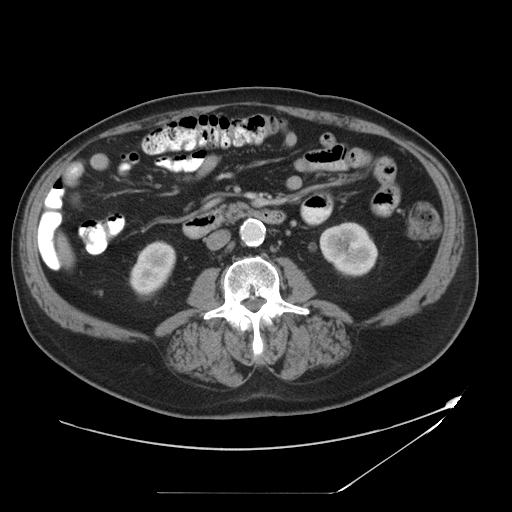
Contrast-enhanced abdominal CT, one axial slice. Position 10 of 49 along the scan axis. 120 kVp. Intravenous contrast given. Soft-tissue window (W 400 / L 40 HU). 512 × 512 image matrix, field of view 461 × 461 mm. Male patient, age 72 years. Case-level facts recorded for this patient, not image findings: diagnosis: colorectal cancer liver metastases, imaged before liver resection; multiple liver metastases: no; largest metastasis: 2.5 cm; chemotherapy before resection: yes.
Outlined on this slice (outlined manually by an expert reader):
- liver: bounding box [x1, y1, x2, y2] px = [62, 249, 65, 252]
- planned liver remnant (the part of the liver to remain after resection): [63, 244, 66, 252]